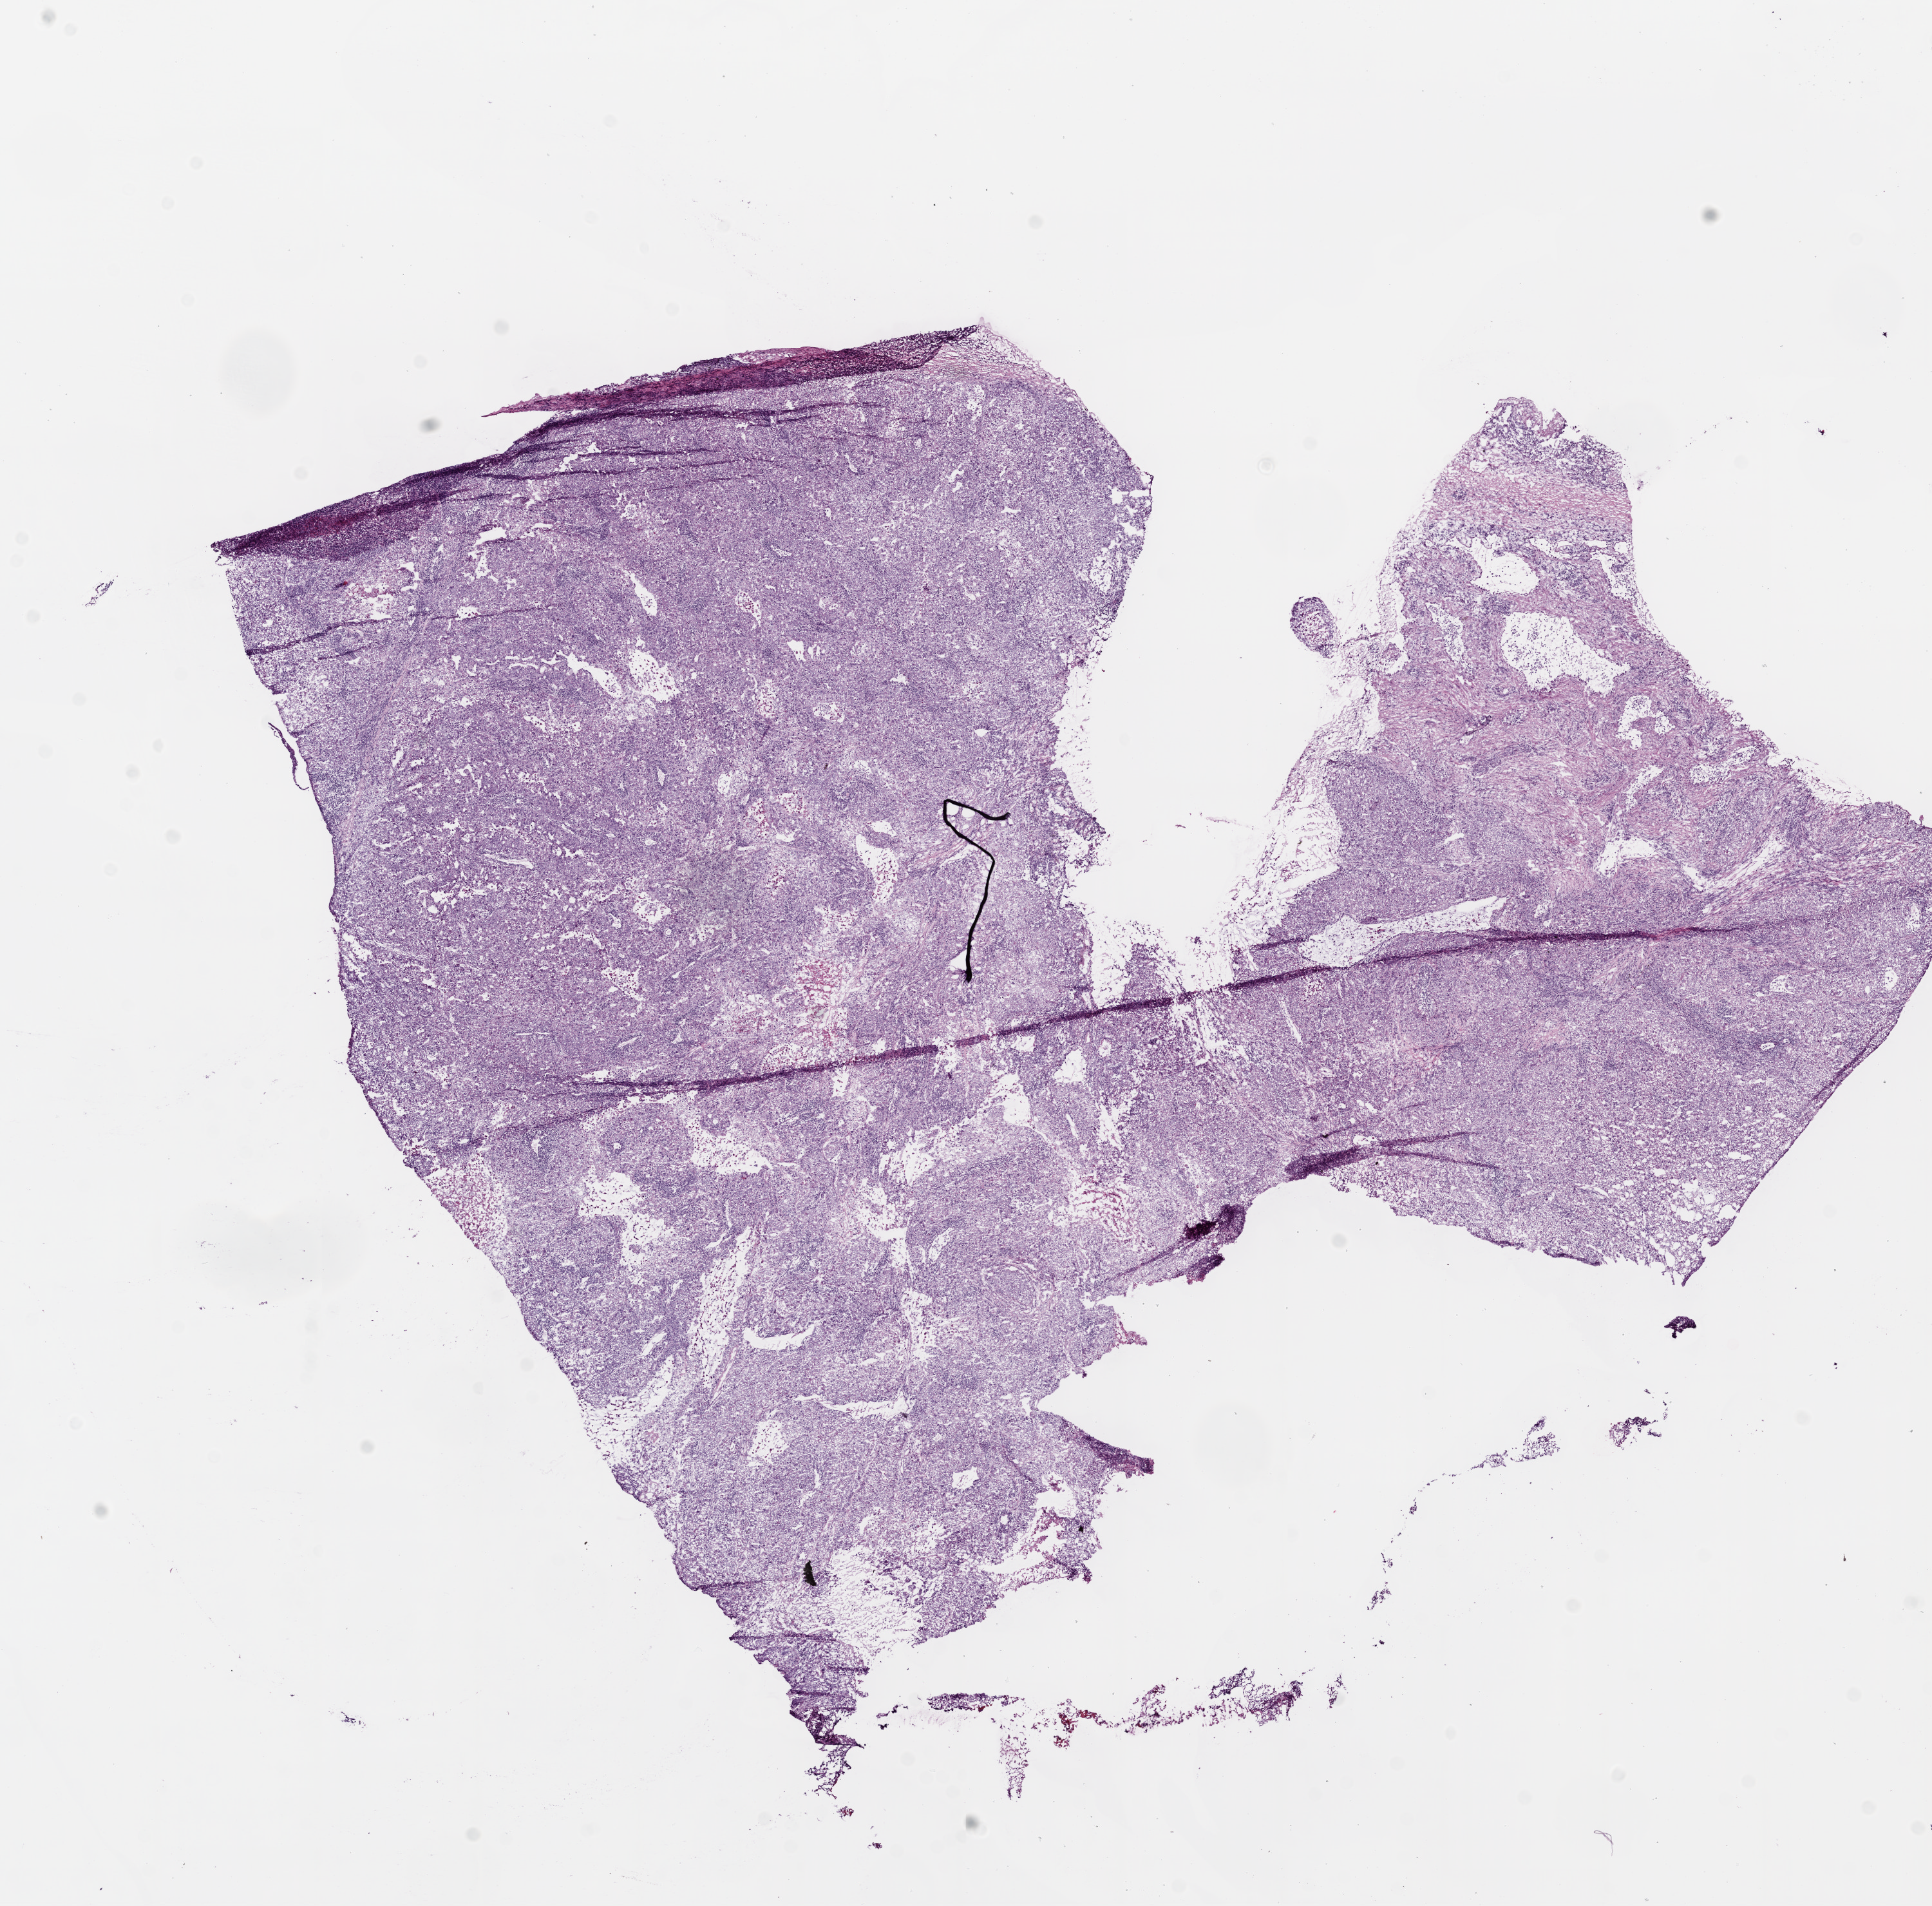
Digitized H&E-stained tissue section (whole slide), low-resolution overview of the scanned area, about 12.0 x 11.9 mm, frozen section from the bottom of the tissue portion, lung, primary tumour sample. Male patient; age at initial diagnosis 69 years. Pathologist review of this section (percent, as recorded): tumour nuclei 75%, normal cells 0%, stromal cells 10%, necrosis 1%.
- diagnosis: Adenocarcinoma with mixed subtypes
- AJCC pathologic stage: IIIA